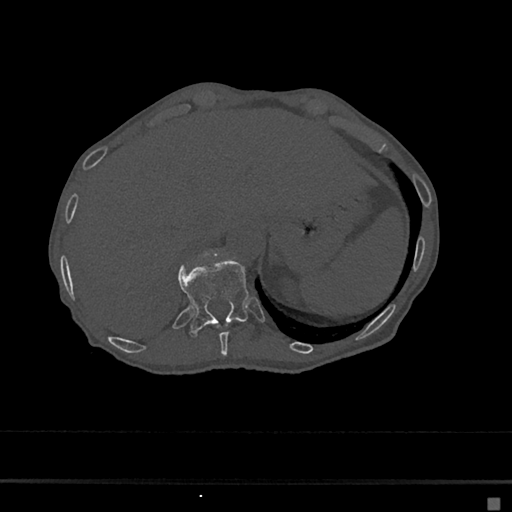
CT including the spine, one axial slice; slice 185 of 797 in the series (ordered by position); 120 kVp; bone window (W 1800 / L 400 HU); 512 × 512 image matrix, field of view 360 × 360 mm. Patient: female, 68 years. Case-level facts recorded for this patient, not image findings: primary cancer: renal.
Outlined on this slice (semi-automatic segmentation, software-assisted and operator-edited):
- T10 vertebra: bounding box (x1, y1, x2, y2) in pixels: (216, 323, 230, 356)
- T11 vertebra: (178, 259, 249, 337)